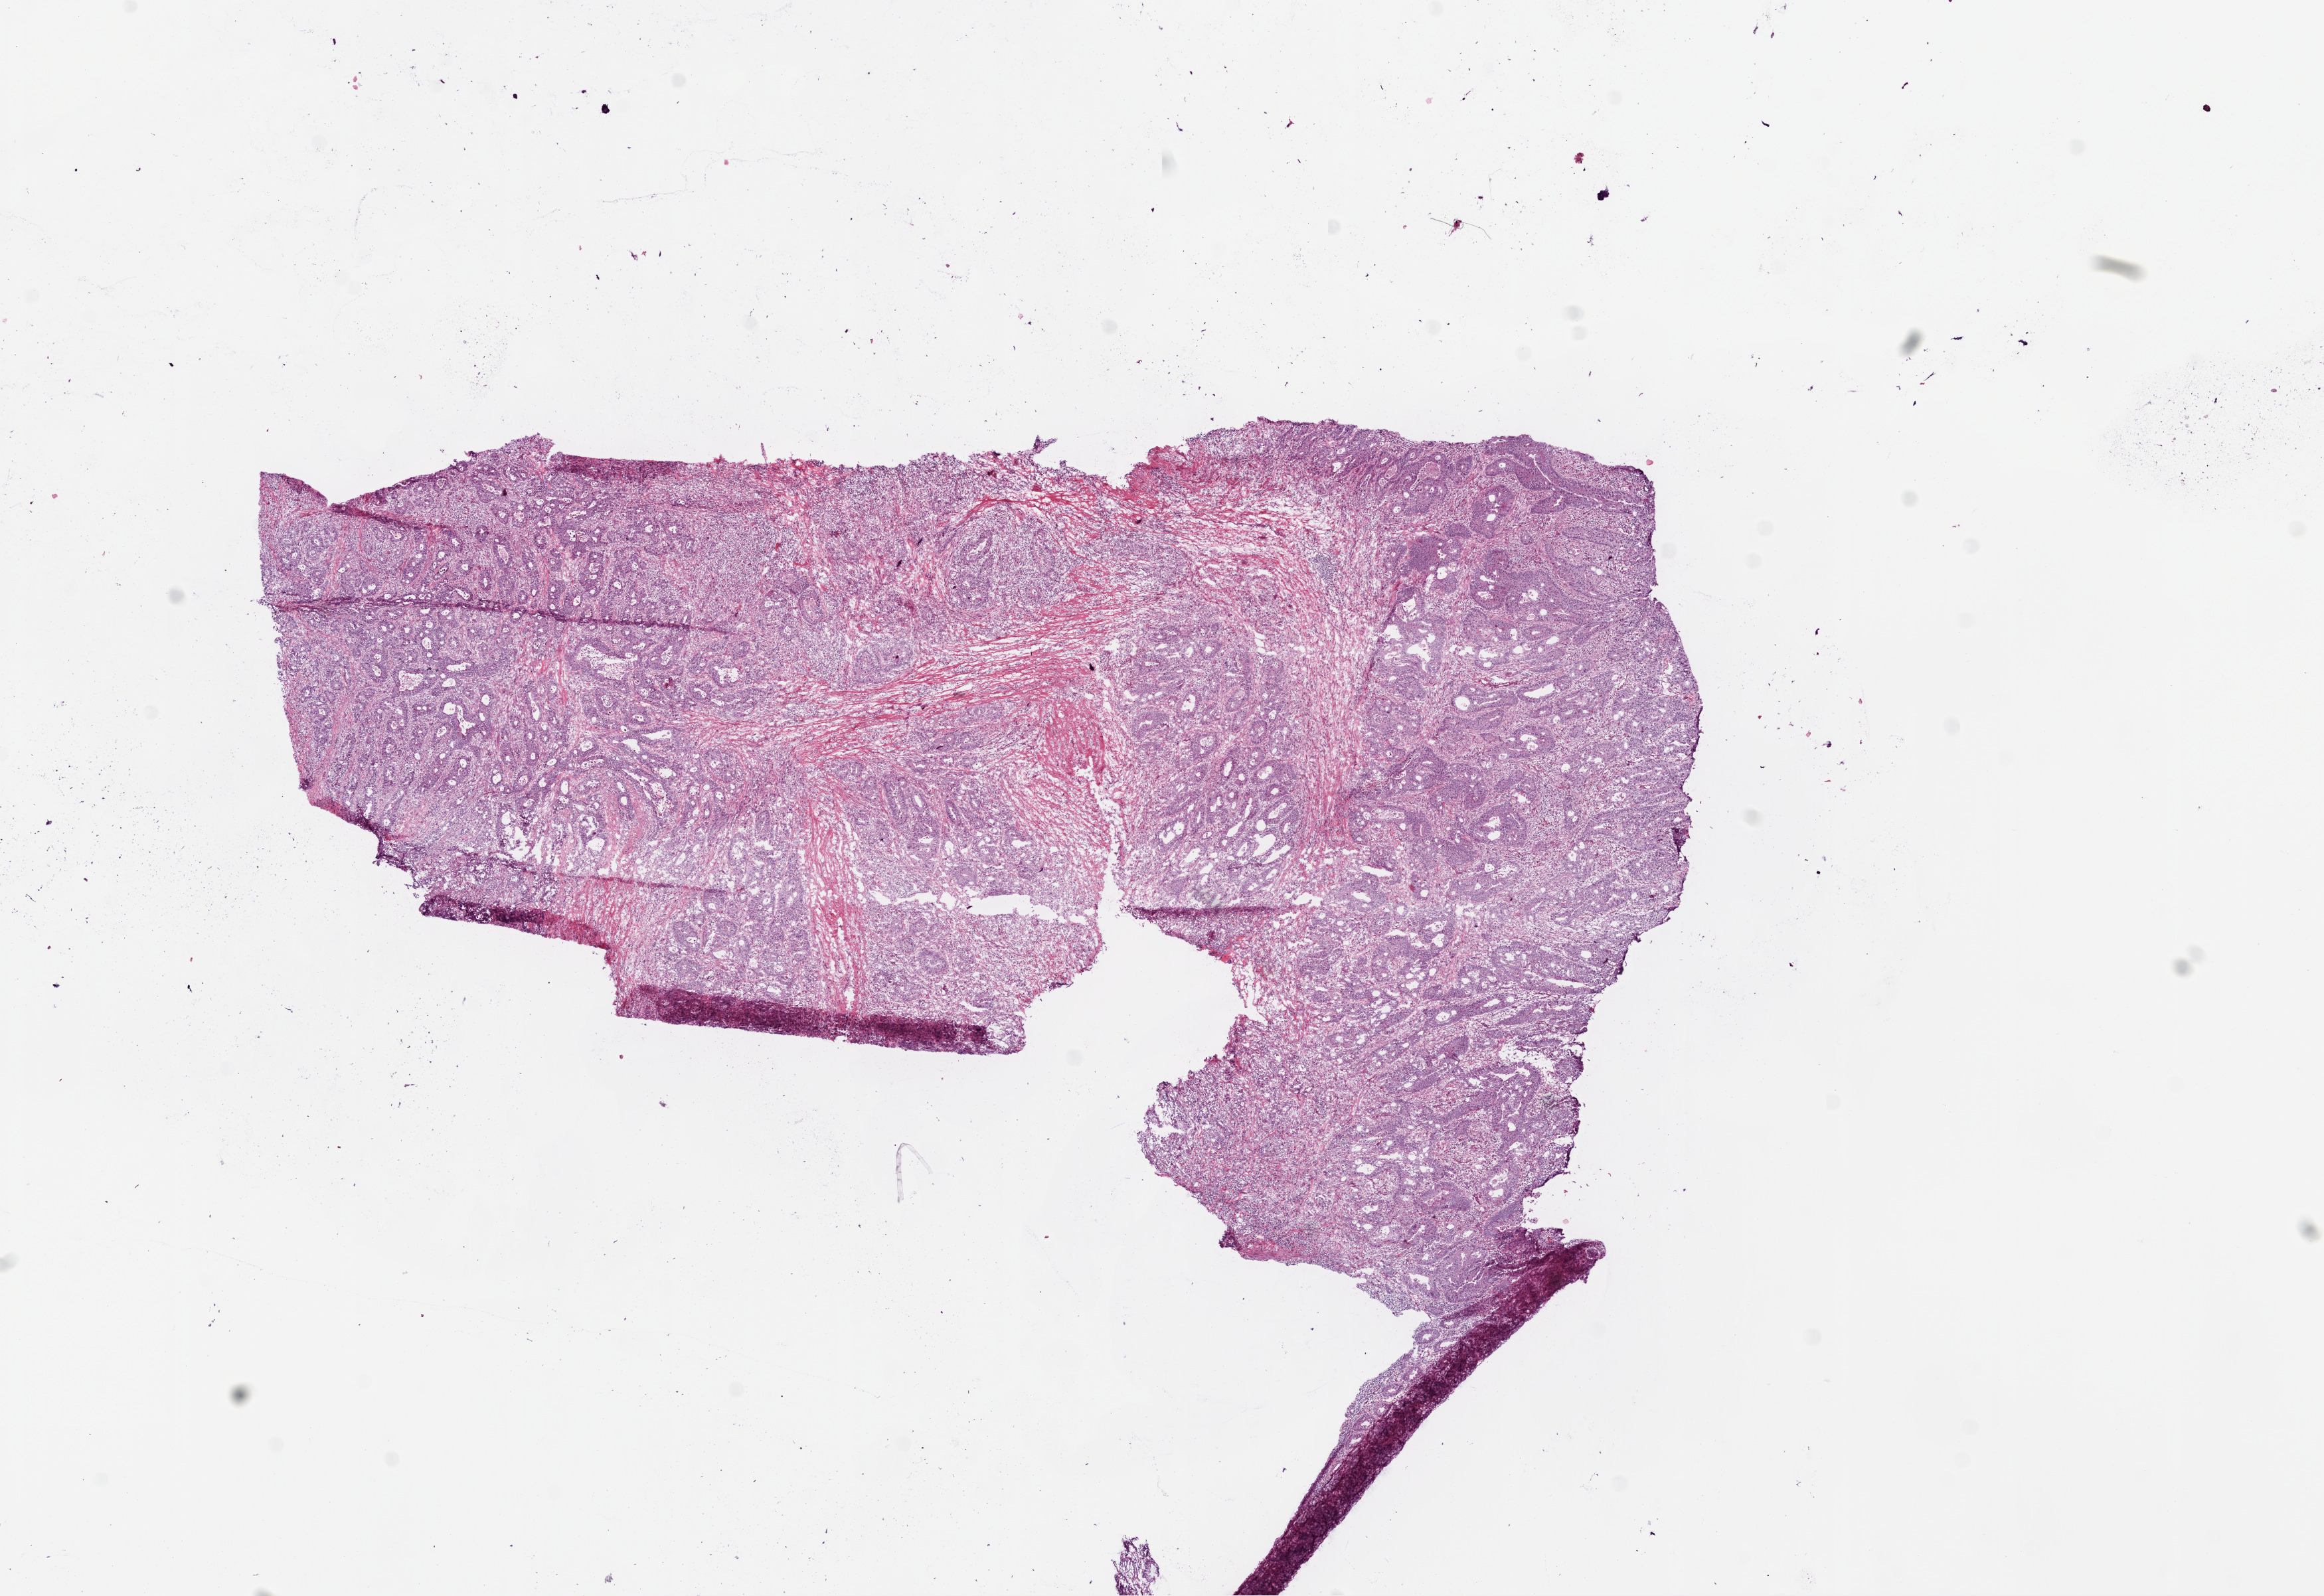
Digitized H&E-stained tissue section (whole slide), whole scanned area (about 14.0 x 9.6 mm) shown as a low-resolution overview; frozen section from the top of the tissue portion; primary tumour sample from the colon. Male patient; age at initial diagnosis 63 years. Composition of this section per pathologist review: tumour cells 75%, tumour nuclei 80%, normal cells 0%, stromal cells 25%, necrosis 0%.
- lymph nodes positive (case pathology): 0 of 35 examined
- pathologic diagnosis: Adenocarcinoma, NOS
- AJCC pathologic stage: IIA (6th edition)